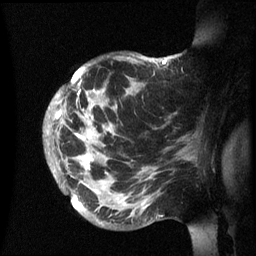
Breast MRI (dynamic contrast-enhanced), one sagittal slice; position 44 of 60 along the scan axis; dynamic contrast-enhanced series, image 2 of 3 at this slice position (ordered by acquisition); 1.5 T; TE 4.2 ms, TR 8.4 ms; 2.4 mm slice thickness; 256 × 256 image matrix. Patient: female, 48 years.
Annotated regions visible in this slice (semi-automatically segmented with operator editing):
- analysis volume of interest (the breast-tissue region the enhancement analysis was run in; not a lesion): bounding box (x1, y1, x2, y2) in pixels: (44, 55, 202, 236)
- tumour enhancement mask (voxels above the 70 % enhancement threshold inside the analysis volume of interest): (47, 57, 172, 174)